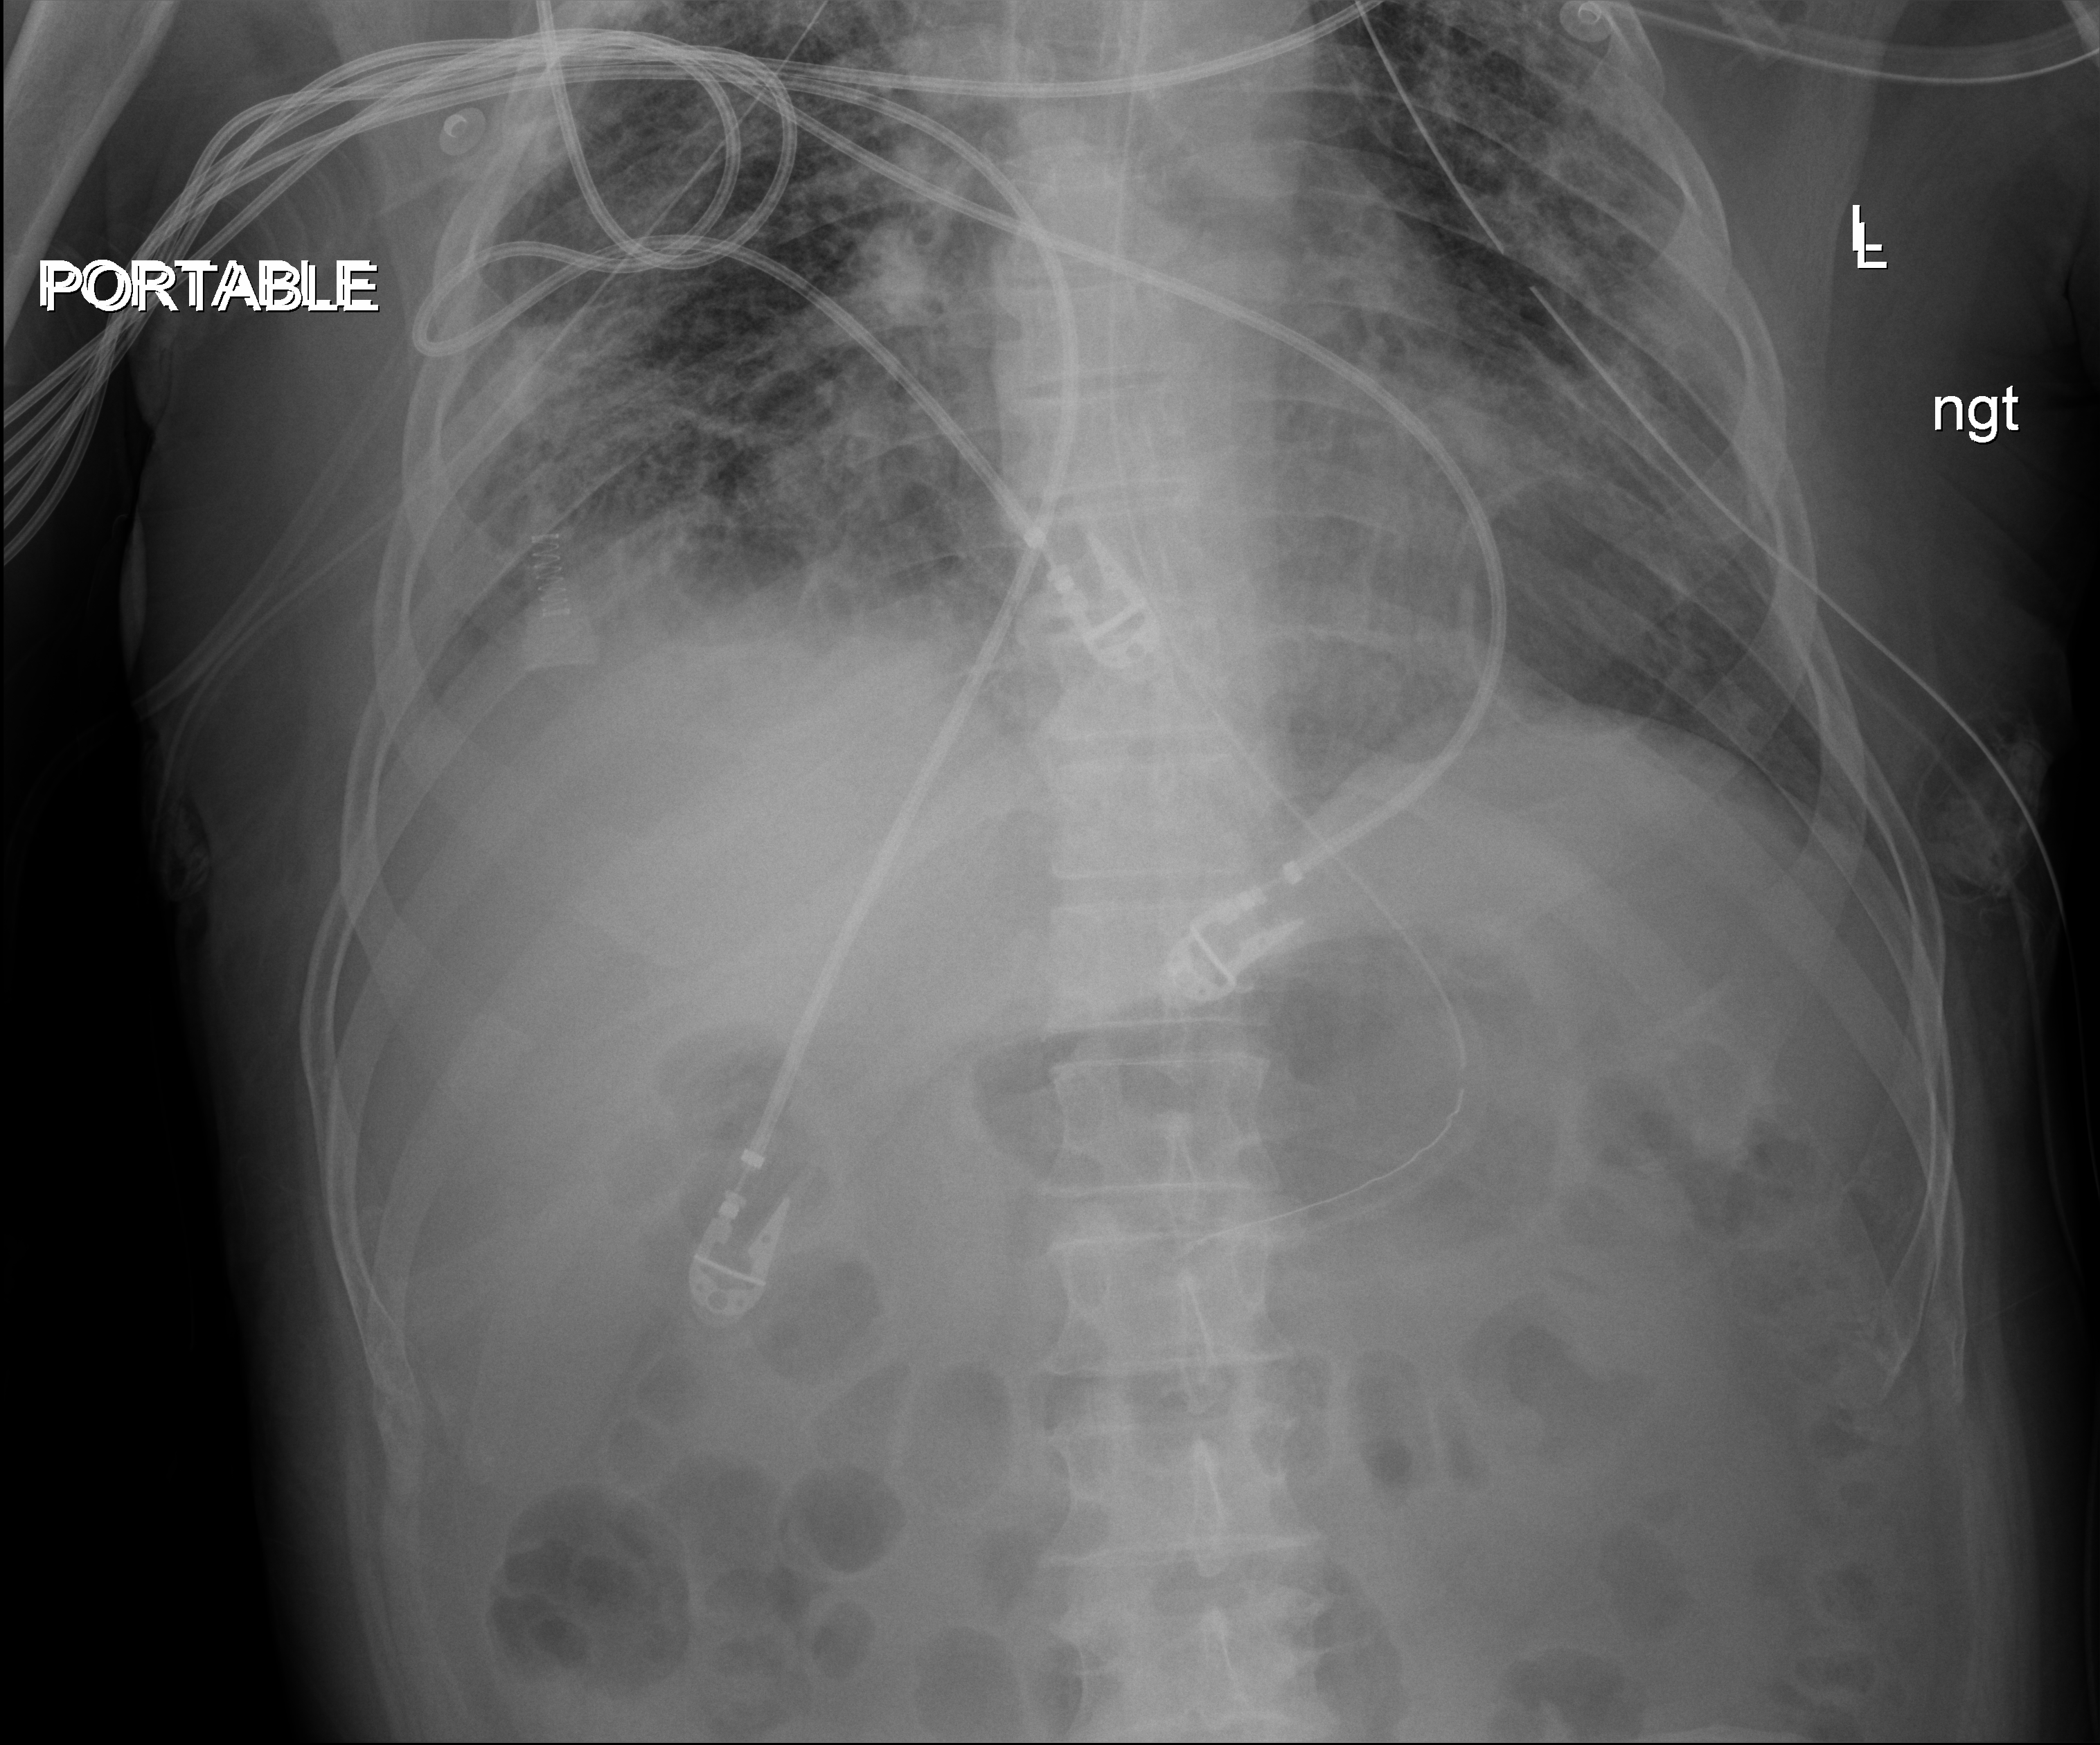
Portable chest radiograph. Male patient hospitalised with COVID-19, age 18–59 years.
Hospital-stay facts (about this admission, not read from this image; timing relative to this image not recorded): admitted to intensive care during this hospital stay: yes; mechanically ventilated during this hospital stay: yes; other chronic lung disease (admission record): no.